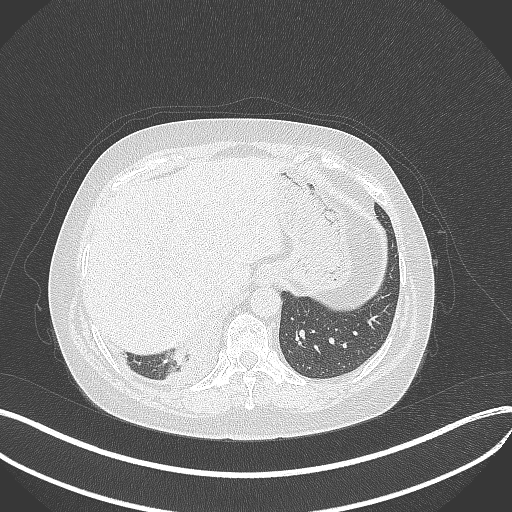
Chest CT, one axial slice; position 72 of 381 along the scan axis; reconstruction kernel B70f; lung window (W 1500 / L -600 HU); 1 mm slice thickness; 512 × 512 image matrix. Female patient, age 56 years. From the clinical record (not read from this slice): clinical TNM (as recorded): T2b N1 M0; histopathological grade: G3.
Outlined on this slice (bounding box drawn by a radiologist):
- lung tumour (recorded histology: small cell carcinoma): bounding box [x1, y1, x2, y2] px = [169, 343, 195, 370]